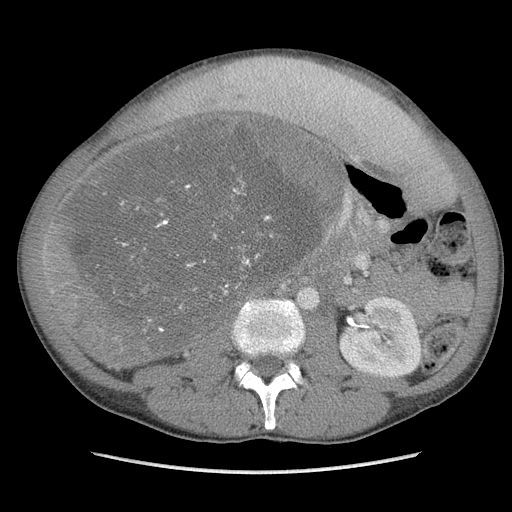
Contrast-enhanced abdominal CT, one axial slice; slice 53 of 115 in the series (ordered by position); soft-tissue window (W 400 / L 40 HU); 512 × 512 image matrix. Male patient. Case-level facts recorded for this patient, not image findings: diagnosis: adrenocortical carcinoma; tumour side: right adrenal; Ki-67 index: 13 %; stage (as recorded): 3.
Annotated regions visible in this slice (semi-automatic segmentation, software-assisted and operator-edited):
- mass: box from (x=48, y=118) to (x=332, y=367) px